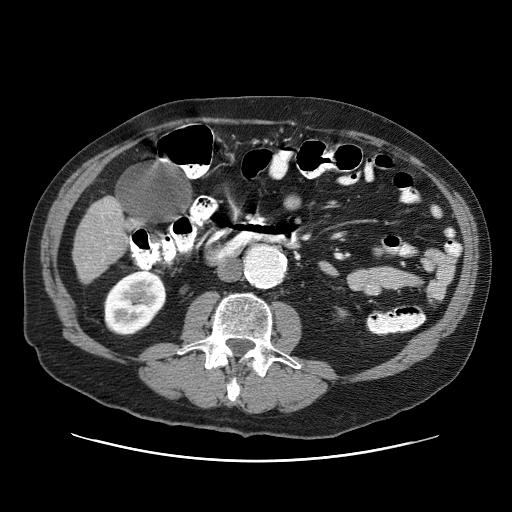
Contrast-enhanced abdominal CT (liver protocol), one axial slice; slice 8 of 87 in the series (ordered by position); 120 kVp; one of 3 acquisitions stored at this slice position; soft-tissue window (W 400 / L 40 HU); 2.5 mm slice thickness; 512 × 512 image matrix, field of view 400 × 400 mm. Case-level facts recorded for this patient, not image findings: diagnosis: hepatocellular carcinoma (patient treated with transarterial chemoembolisation; whether this scan precedes or follows treatment is not stated here); TNM stage (as recorded): Stage-IIIA; Child-Pugh class: A; tumour differentiation: well differentiated.
Annotated regions visible in this slice (semi-automatic segmentation, software-assisted and operator-edited):
- liver parenchyma outside the tumour (the mass and vessels are separate outlines, so this box may not span the whole liver): bounding box (x1, y1, x2, y2) in pixels: (72, 196, 126, 282)